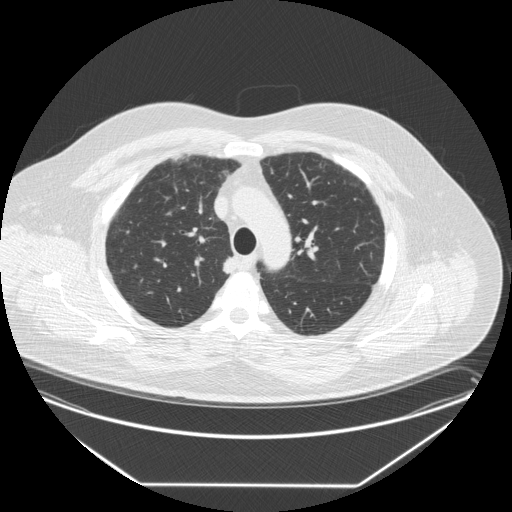
Chest CT (low-dose screening protocol), one axial image; third screening round (two years after baseline); lung window (W 1500 / L -600 HU); 2.5 mm slice thickness; 120 kVp; slice 57 of 258 in the series; 512 × 512 image matrix. Male, age 58 years at enrolment. Former smoker at enrolment.
• Expert-annotated lung lesion, bounding box [x1, y1, x2, y2] px = [215, 252, 248, 284].
• The exam's reader record, not a measurement of the box and not confirmed to be the same lesion: non-calcified nodule or mass ≥4 mm, right upper lobe, 15 × 12 mm, smooth margins, soft tissue attenuation, pre-existing on the prior screen: no.
• Official screen result: positive, other.
• Lung cancer was diagnosed 17 days after this screen: large cell carcinoma, NOS, right upper lobe, stage IV (AJCC 6th edition), 35 mm at pathology.